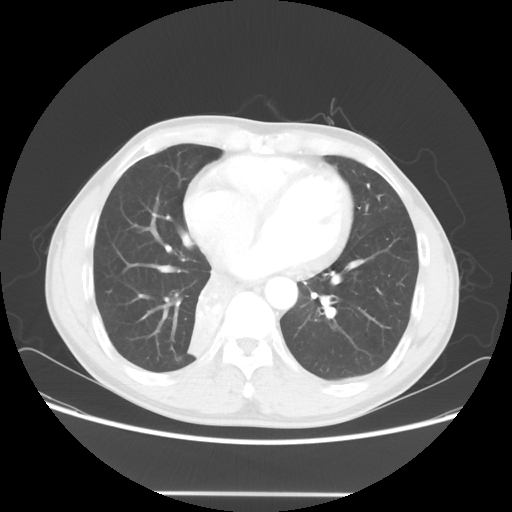
Chest CT, one axial slice; 120 kVp; lung window (W 1500 / L -600 HU); 5 mm slice thickness; 512 × 512 image matrix, field of view 393 × 393 mm. Male patient, age 47 years. Case-level facts recorded for this patient, not image findings: clinical TNM (as recorded): T2 N0 M0; histopathological grade: G2.
Structures marked on this image (rectangle marked by the reading radiologist):
- lung tumour (recorded histology: squamous cell carcinoma): bounding box <189,265,235,370> (left, top, right, bottom; pixels)